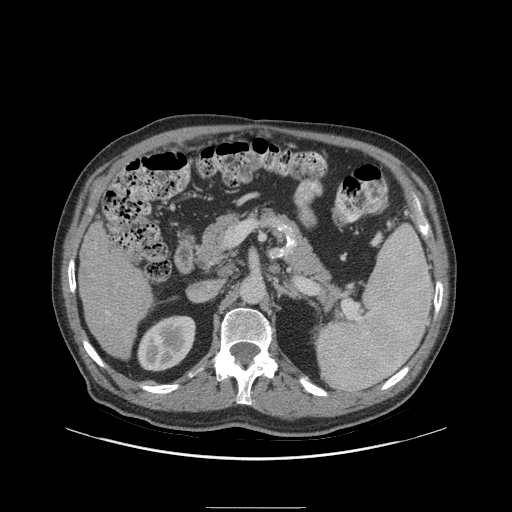
Contrast-enhanced abdominal CT (liver protocol), one axial slice. Position 42 of 105 along the scan axis. Reconstruction kernel STANDARD. 140 kVp. Soft-tissue window (W 400 / L 40 HU). 2.5 mm slice thickness. 512 × 512 image matrix, field of view 440 × 440 mm. Case-level facts recorded for this patient, not image findings: diagnosis: hepatocellular carcinoma (patient treated with transarterial chemoembolisation; whether this scan precedes or follows treatment is not stated here); TNM stage (as recorded): Stage-I; Child-Pugh class: A; tumour size: 5.1 cm.
Structures marked on this image (semi-automatic segmentation, software-assisted and operator-edited):
- liver parenchyma outside the tumour (the mass and vessels are separate outlines, so this box may not span the whole liver): bounding box <78,222,152,358> (left, top, right, bottom; pixels)